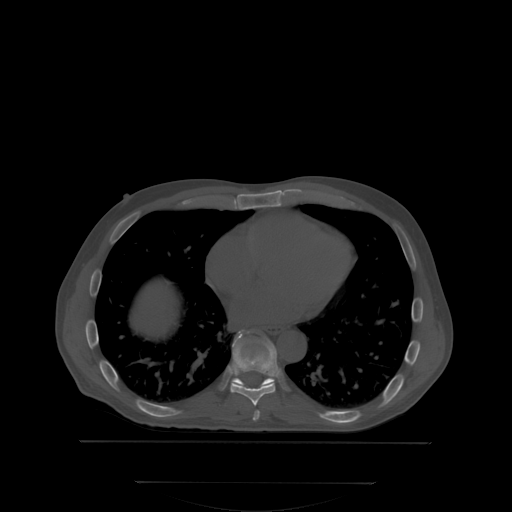
CT including the spine, one axial slice. Position 213 of 350 along the scan axis. Bone window (W 1800 / L 400 HU). 2.5 mm slice thickness. 512 × 512 image matrix, field of view 500 × 500 mm. Patient: male, 58 years. From the clinical record (not read from this slice): primary cancer: prostate; vertebrae with lytic lesions (as recorded): L1.
Structures marked on this image (semi-automatically segmented with operator editing):
- T7 vertebra: bounding box (x1, y1, x2, y2) in pixels: (254, 411, 259, 418)
- T8 vertebra: (230, 331, 278, 405)
- T9 vertebra: (233, 374, 274, 384)